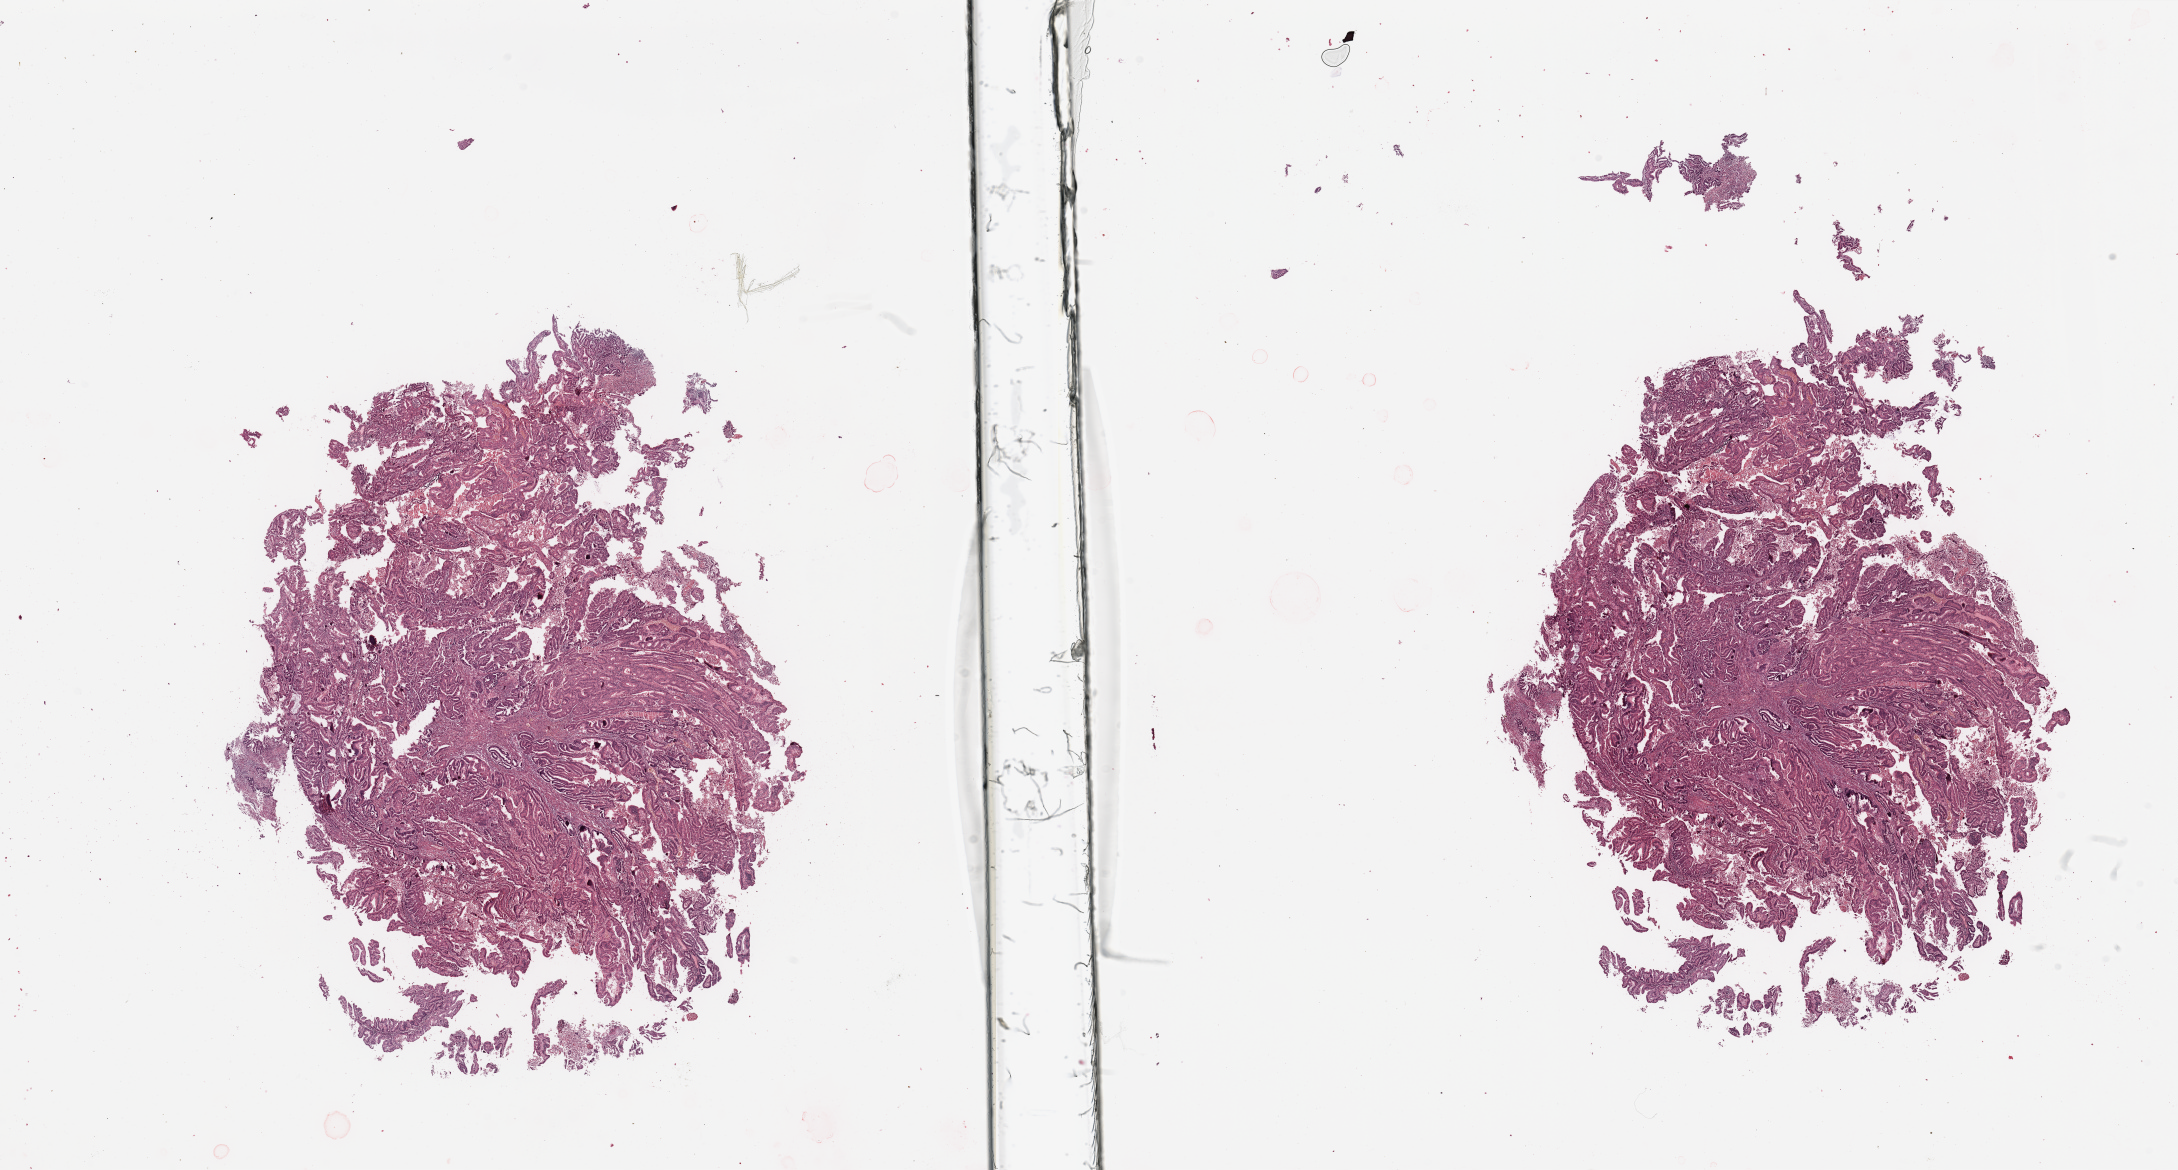
H&E whole-slide image — whole scanned area (about 34.5 x 18.5 mm, acquisition: 20x scan) shown as a low-resolution overview, uterus, tumour tissue. Patient: female, age 54 years. Histologic grade: G2 (moderately differentiated).
• histologic diagnosis: Endometrioid adenocarcinoma, NOS
• AJCC pathologic stage: I